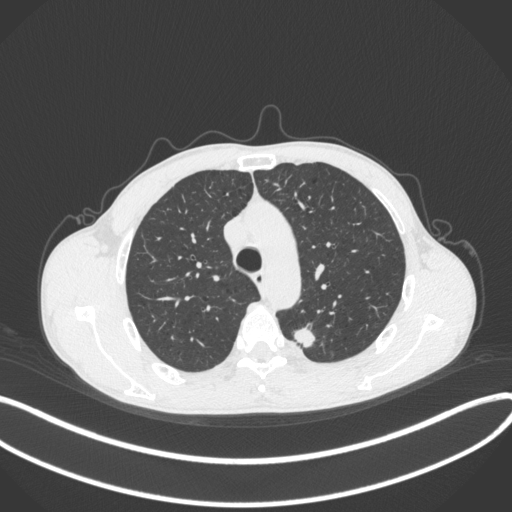
Chest CT, one axial slice. Slice 293 of 429 in the series (ordered by position). Reconstruction kernel B31f. 120 kVp. Lung window (W 1500 / L -600 HU). 1 mm slice thickness. 512 × 512 image matrix, field of view 400 × 400 mm. Male patient, age 51 years. Case-level facts recorded for this patient, not image findings: clinical TNM (as recorded): T2a N1 M1.
Annotated regions visible in this slice (rectangle marked by the reading radiologist):
- lung tumour (recorded histology: adenocarcinoma): bounding box <290,322,319,353> (left, top, right, bottom; pixels)